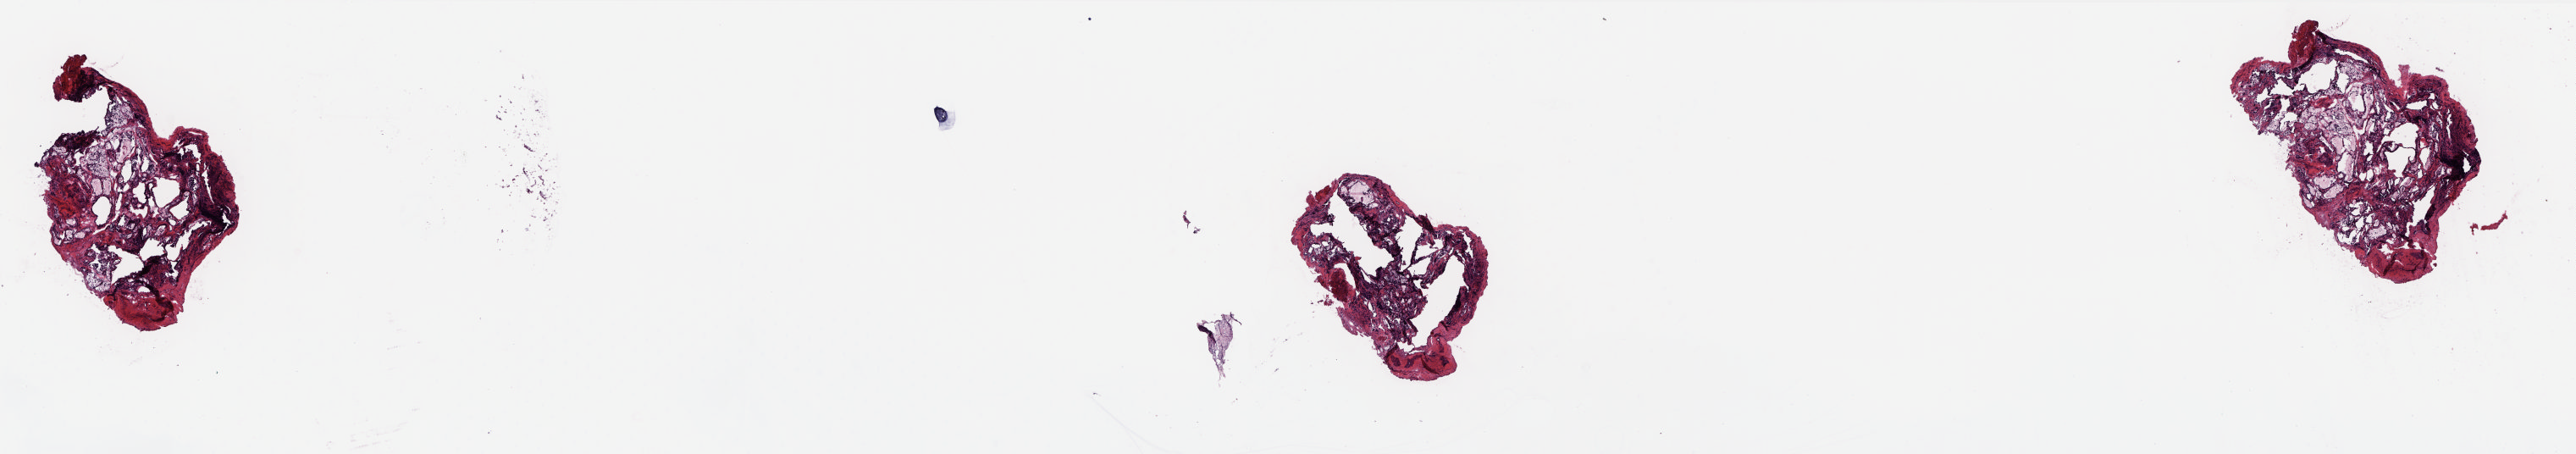
Hematoxylin and eosin (H&E) stained whole-slide image — shown as a low-resolution overview of the whole scanned area (about 24.5 x 4.3 mm). Frozen section from the top of the tissue portion. Sample: solid tissue normal (non-tumour tissue), thyroid. Female, age 43 years at initial diagnosis. Composition of this section per pathologist review: tumour cells 0%, tumour nuclei 0%, normal cells 75%, stromal cells 25%, necrosis 0%. Infiltration values recorded for this section: lymphocyte infiltration 5%, monocyte infiltration 5%, neutrophil infiltration 0%.
- this section: solid tissue normal sample (biorepository sample class)
- patient diagnosis: Papillary adenocarcinoma, NOS